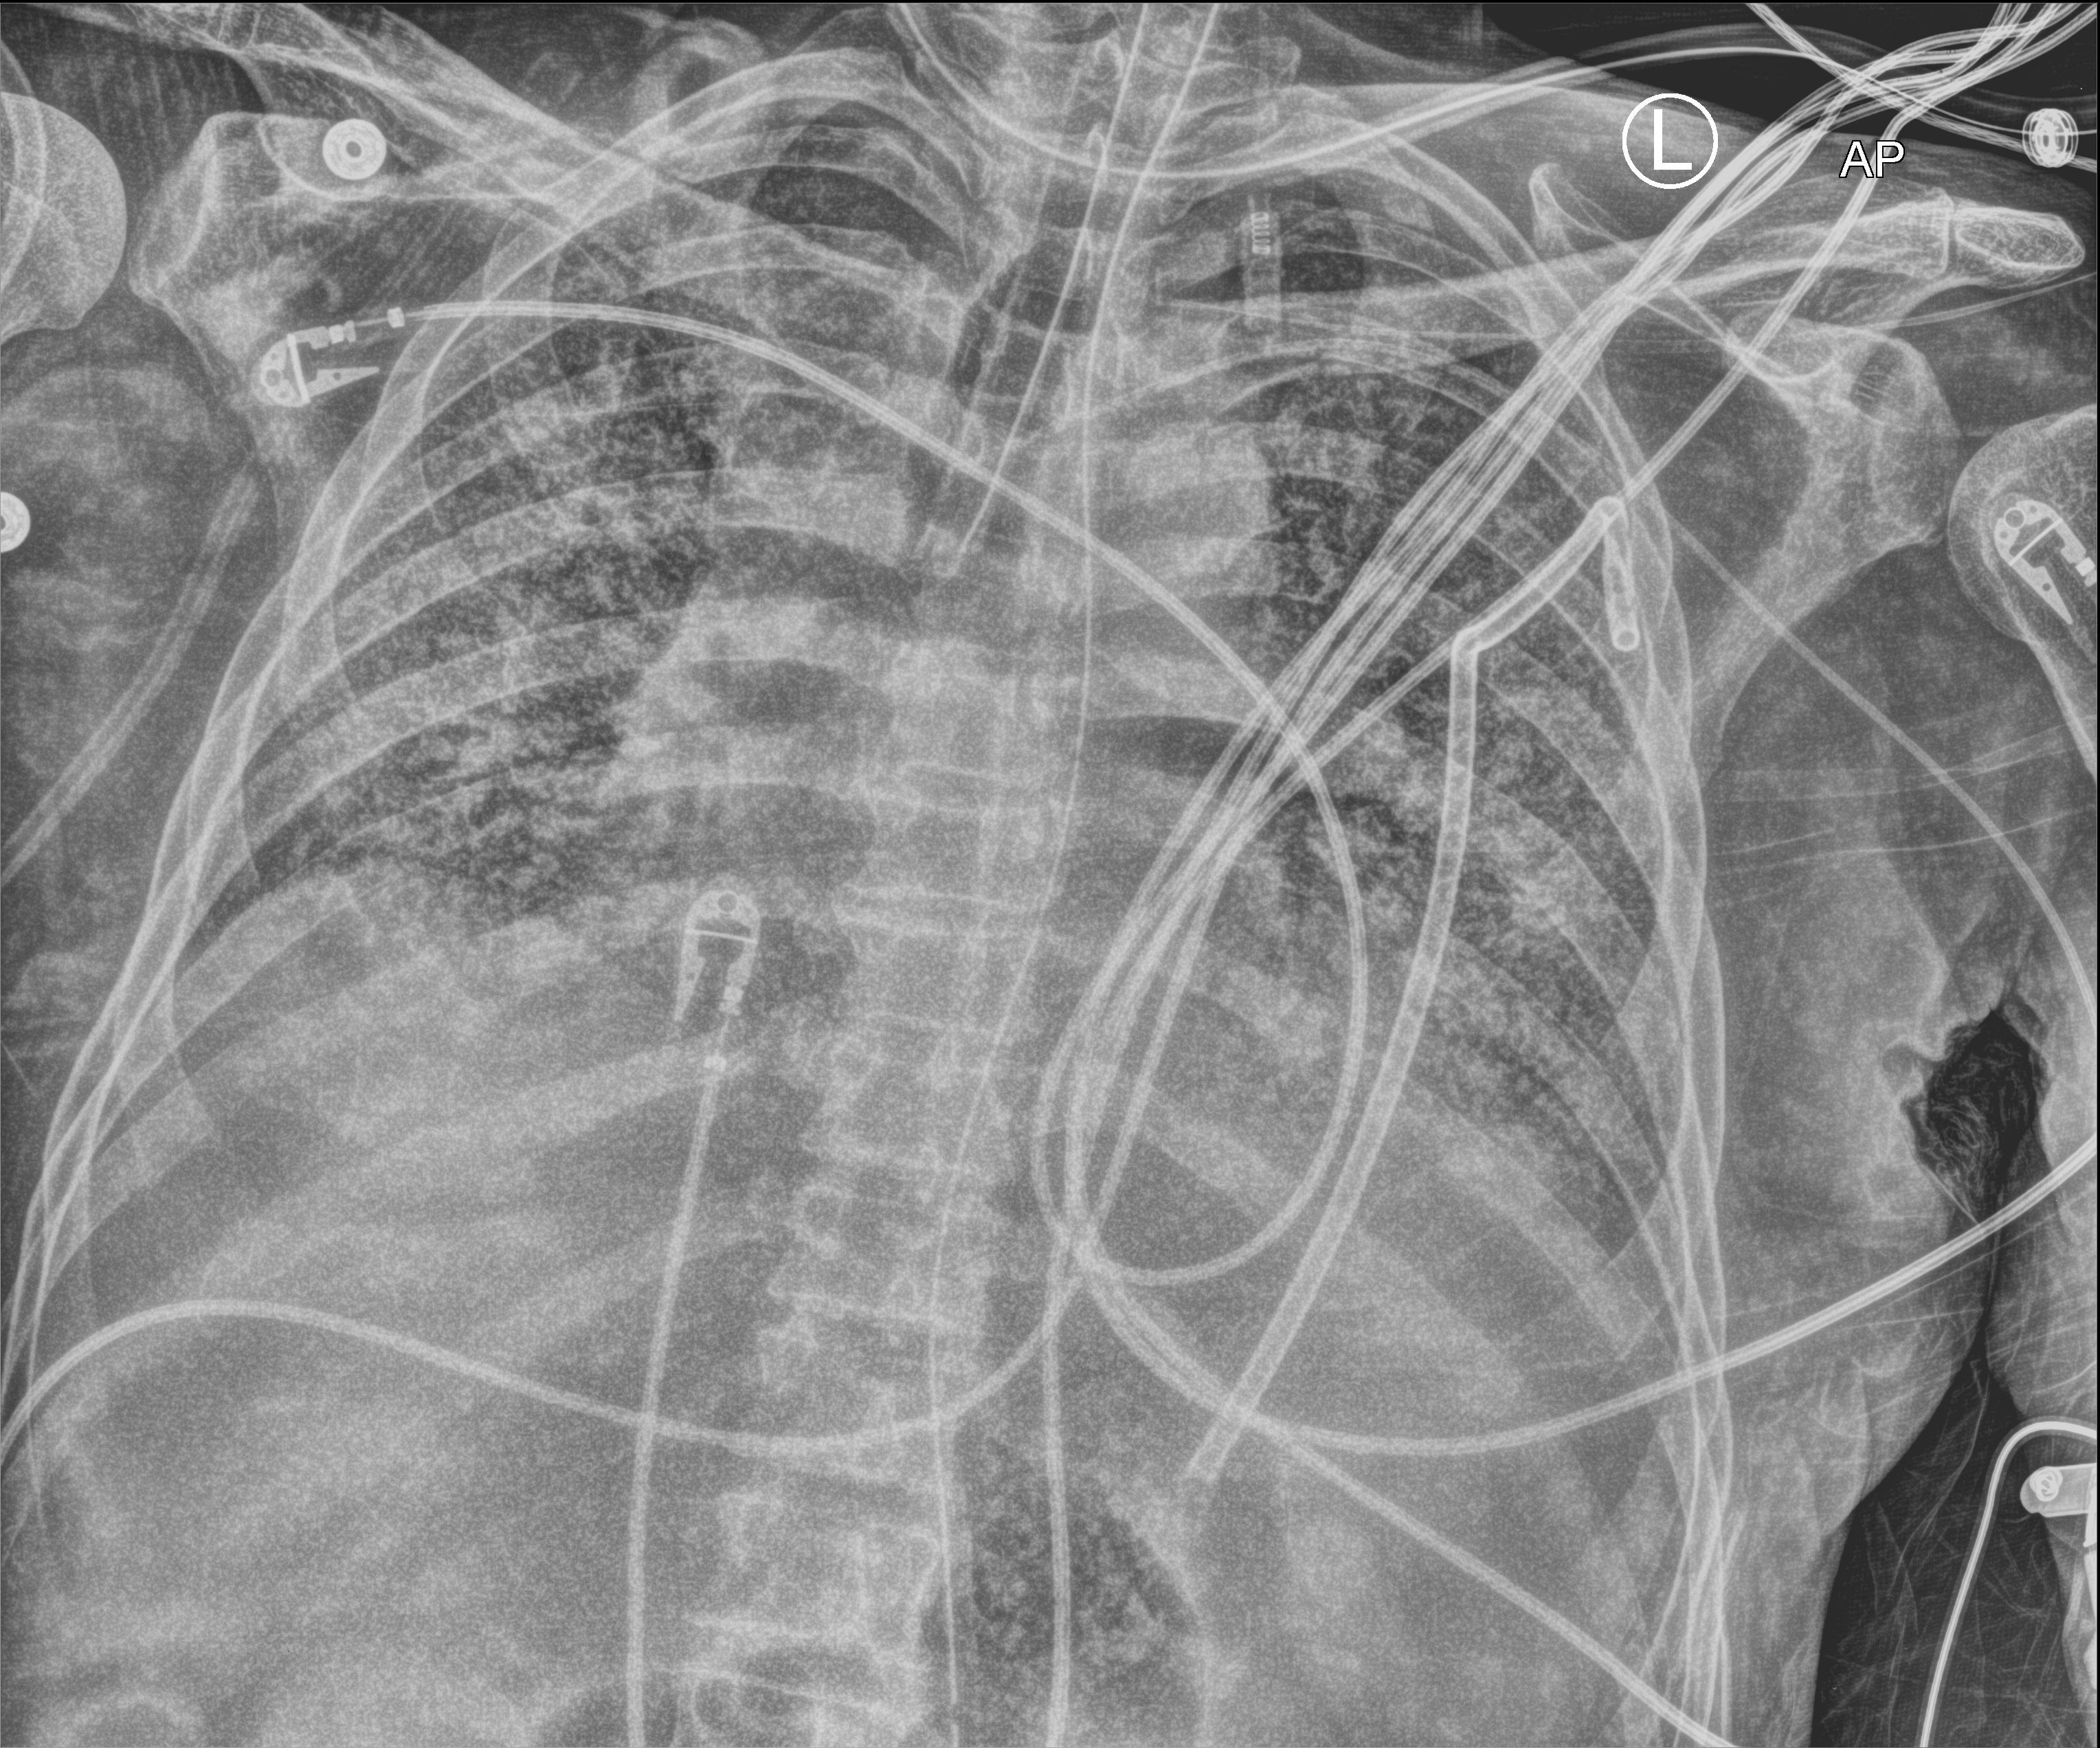
Bedside chest radiograph (computed radiography). Patient hospitalised with COVID-19; male, aged 60–74 years.
From the hospital-stay record, not from the radiograph (when in the stay this image was taken is not recorded):
- length of hospital stay: 54 days
- mechanically ventilated during this hospital stay: yes
- admitted to intensive care during this hospital stay: yes